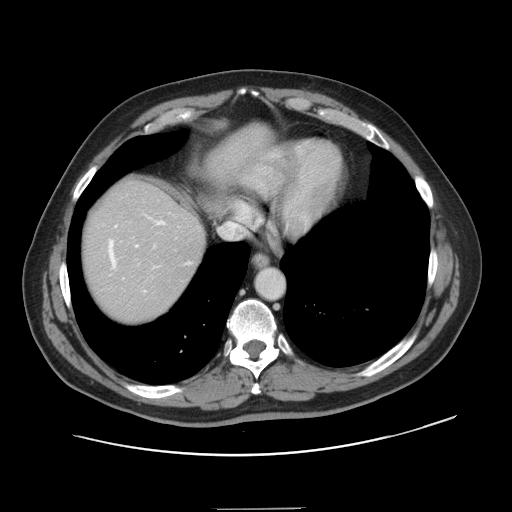
Contrast-enhanced abdominal CT, one axial slice. Position 129 of 143 along the scan axis. Intravenous contrast given. Soft-tissue window (W 400 / L 40 HU). 2.5 mm slice thickness. 512 × 512 image matrix, field of view 402 × 402 mm. Male patient, age 62 years. From the clinical record (not read from this slice): diagnosis: colorectal cancer liver metastases, imaged before liver resection; multiple liver metastases: yes; largest metastasis: 2.7 cm; disease in both lobes: no.
Annotated regions visible in this slice (expert manual segmentation):
- hepatic veins: bounding box (x1, y1, x2, y2) in pixels: (109, 220, 189, 292)
- liver: (82, 127, 267, 322)
- planned liver remnant (the part of the liver to remain after resection): (82, 127, 267, 300)